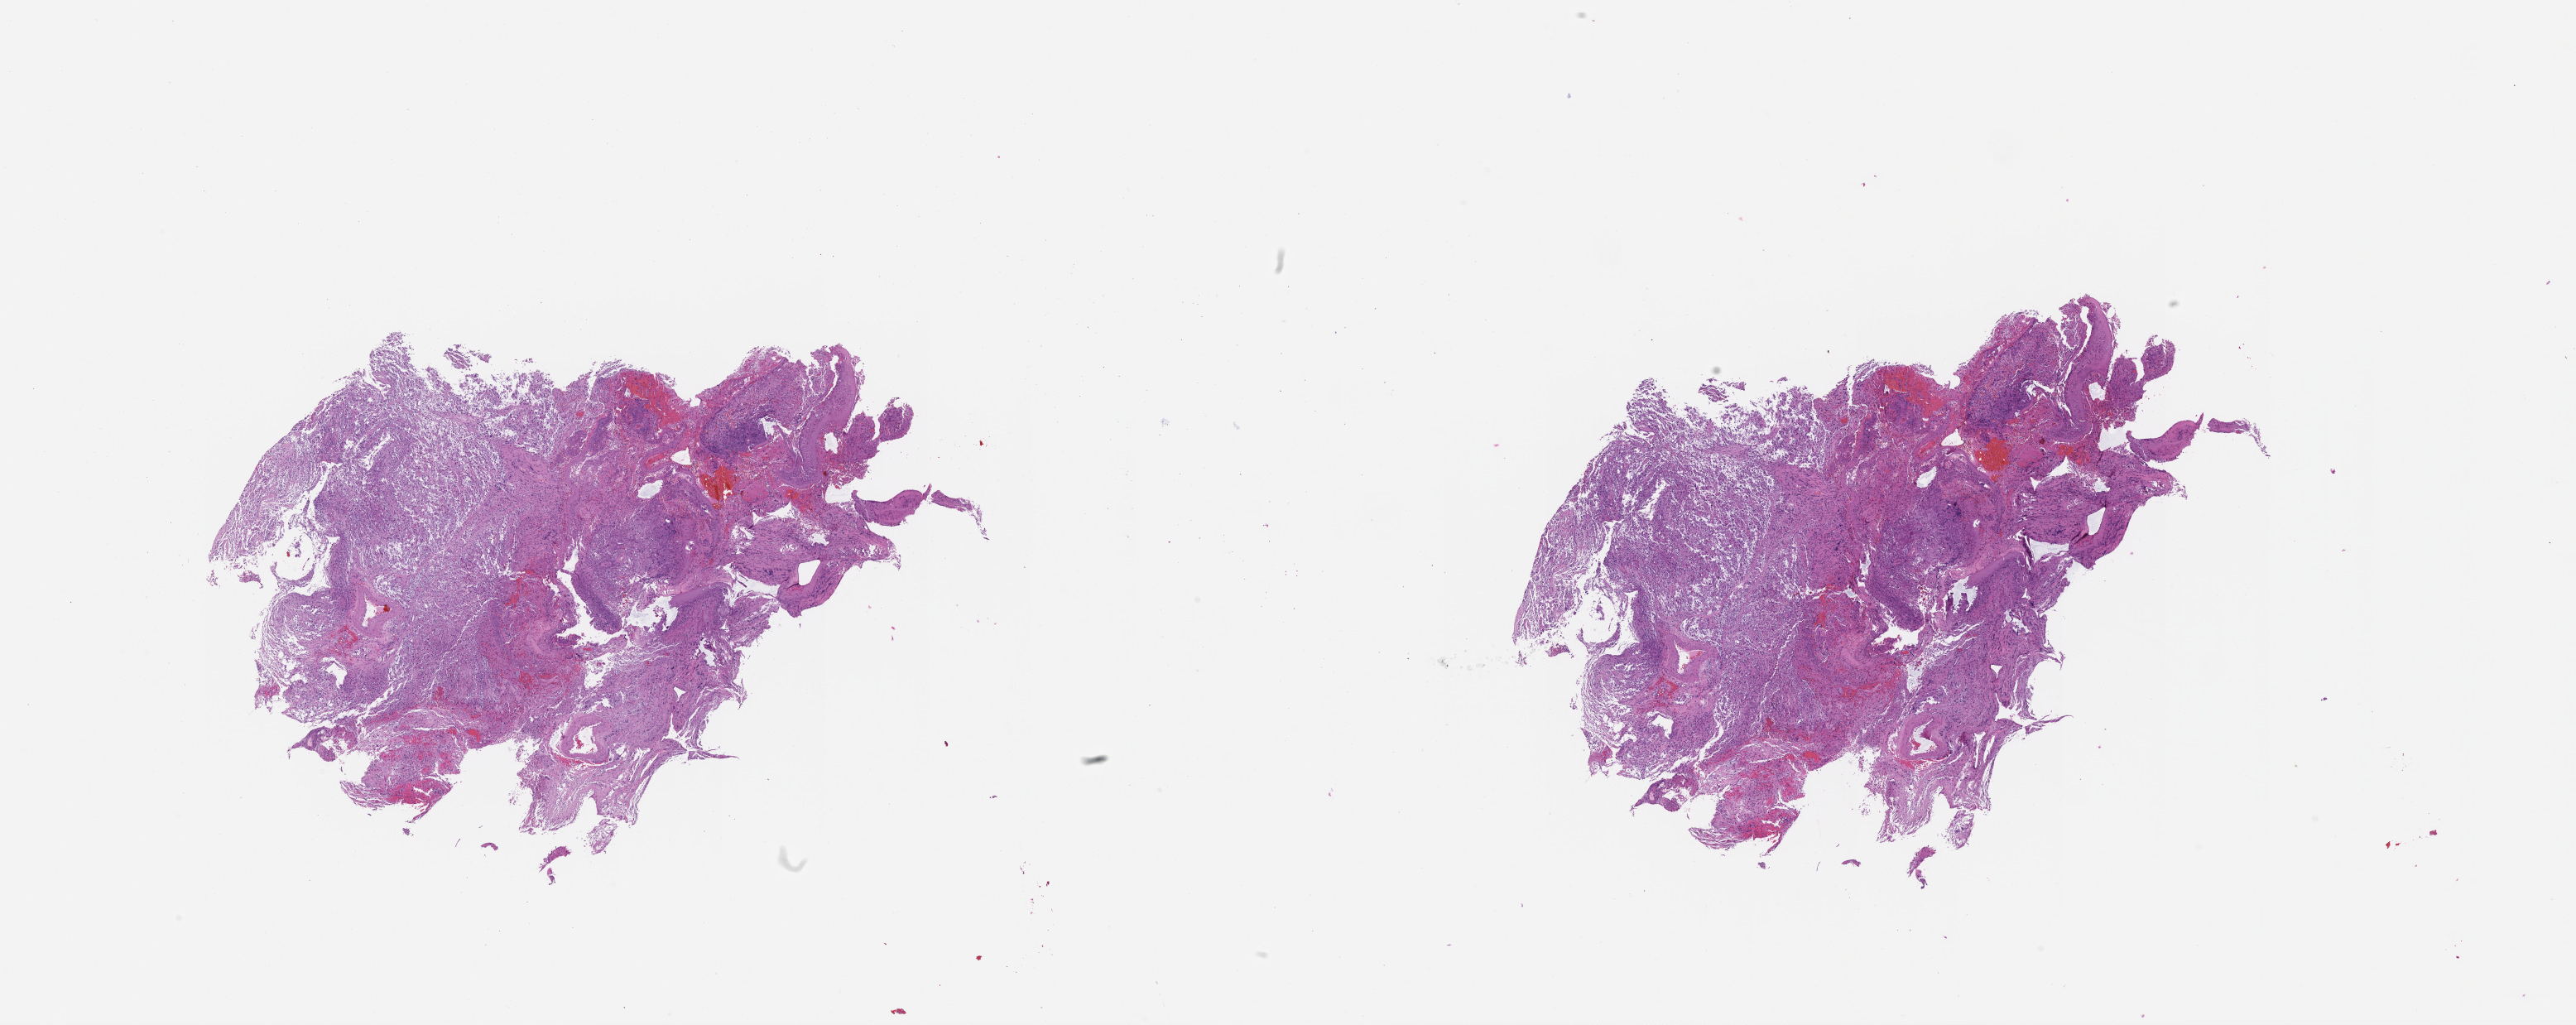
Whole-slide histology image, Hematoxylin and eosin (H&E) stained, whole scanned area (about 25.1 x 10.0 mm) shown as a low-resolution overview, tumour tissue sample, sampled site: brain. Male, 74 y/o. Pathologist review of this section (percent, as recorded): tumour nuclei 80%, necrosis 10%.
Diagnosis: Glioblastoma. Primary tumour site (as recorded): temporal lobe.